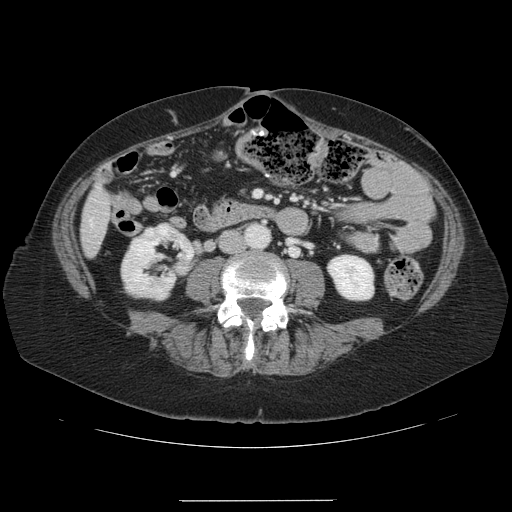
Contrast-enhanced abdominal CT, one axial slice. Slice 17 of 141 in the series (ordered by position). 120 kVp. Intravenous contrast given. Soft-tissue window (W 400 / L 40 HU). 512 × 512 image matrix, field of view 393 × 393 mm. Female patient, age 74 years. Case-level facts recorded for this patient, not image findings: diagnosis: colorectal cancer liver metastases, imaged before liver resection; multiple liver metastases: yes; largest metastasis: 7 cm; chemotherapy before resection: no.
Annotated regions visible in this slice (outlined manually by an expert reader):
- liver: box from (x=82, y=188) to (x=111, y=255) px
- planned liver remnant (the part of the liver to remain after resection): (x=87, y=188)–(x=111, y=228)